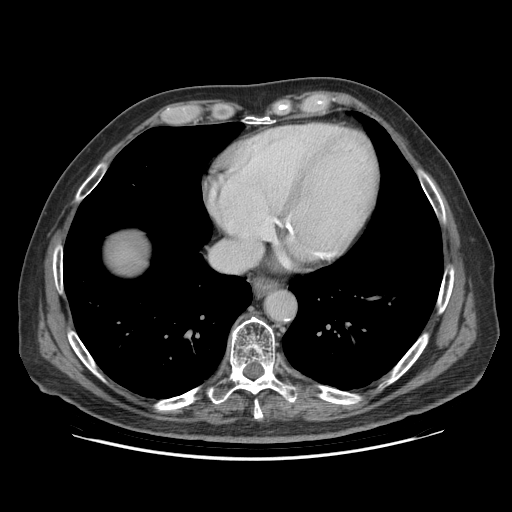
Contrast-enhanced abdominal CT (liver protocol), one axial slice; slice 85 of 95 in the series (ordered by position); 140 kVp; soft-tissue window (W 400 / L 40 HU); 2.5 mm slice thickness; 512 × 512 image matrix, field of view 400 × 400 mm. From the clinical record (not read from this slice): diagnosis: hepatocellular carcinoma (patient treated with transarterial chemoembolisation; whether this scan precedes or follows treatment is not stated here); TNM stage (as recorded): Stage-IVB; Child-Pugh class: A; tumour nodularity: uninodular.
Structures marked on this image (semi-automatic segmentation, software-assisted and operator-edited):
- liver parenchyma outside the tumour (the mass and vessels are separate outlines, so this box may not span the whole liver): bounding box (x1, y1, x2, y2) in pixels: (110, 236, 146, 272)